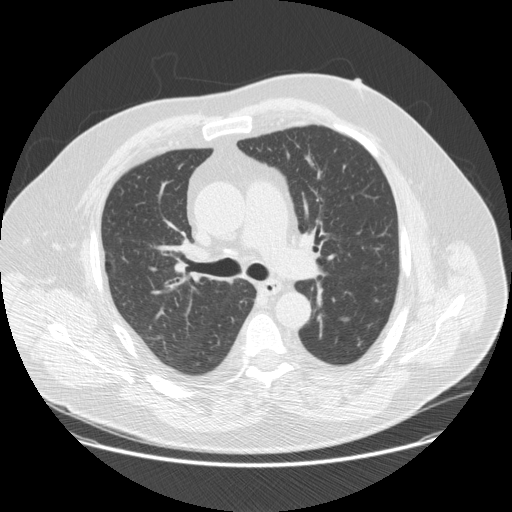
Axial slice from a low-dose chest CT screening exam. Second annual screen. Lung window (W 1500 / L -600 HU). 2.5 mm slice thickness. Standard (soft-tissue) reconstruction kernel (STANDARD). Slice 52 of 172 in the series. Male participant, aged 69 years at enrolment.
Lesion marked by an expert reader, bounding box (x1, y1, x2, y2) in pixels: (346, 332, 371, 358). Screening reader's record for this exam: no non-calcified nodule ≥4 mm recorded. Official screen result: negative screen, minor abnormalities not suspicious for lung cancer. Later outcome: lung cancer diagnosed 534 days after this screen (after the third annual screen) — squamous cell carcinoma, NOS, left lower lobe, moderately differentiated (G2), stage IA (AJCC 6th edition), 14 mm at pathology.